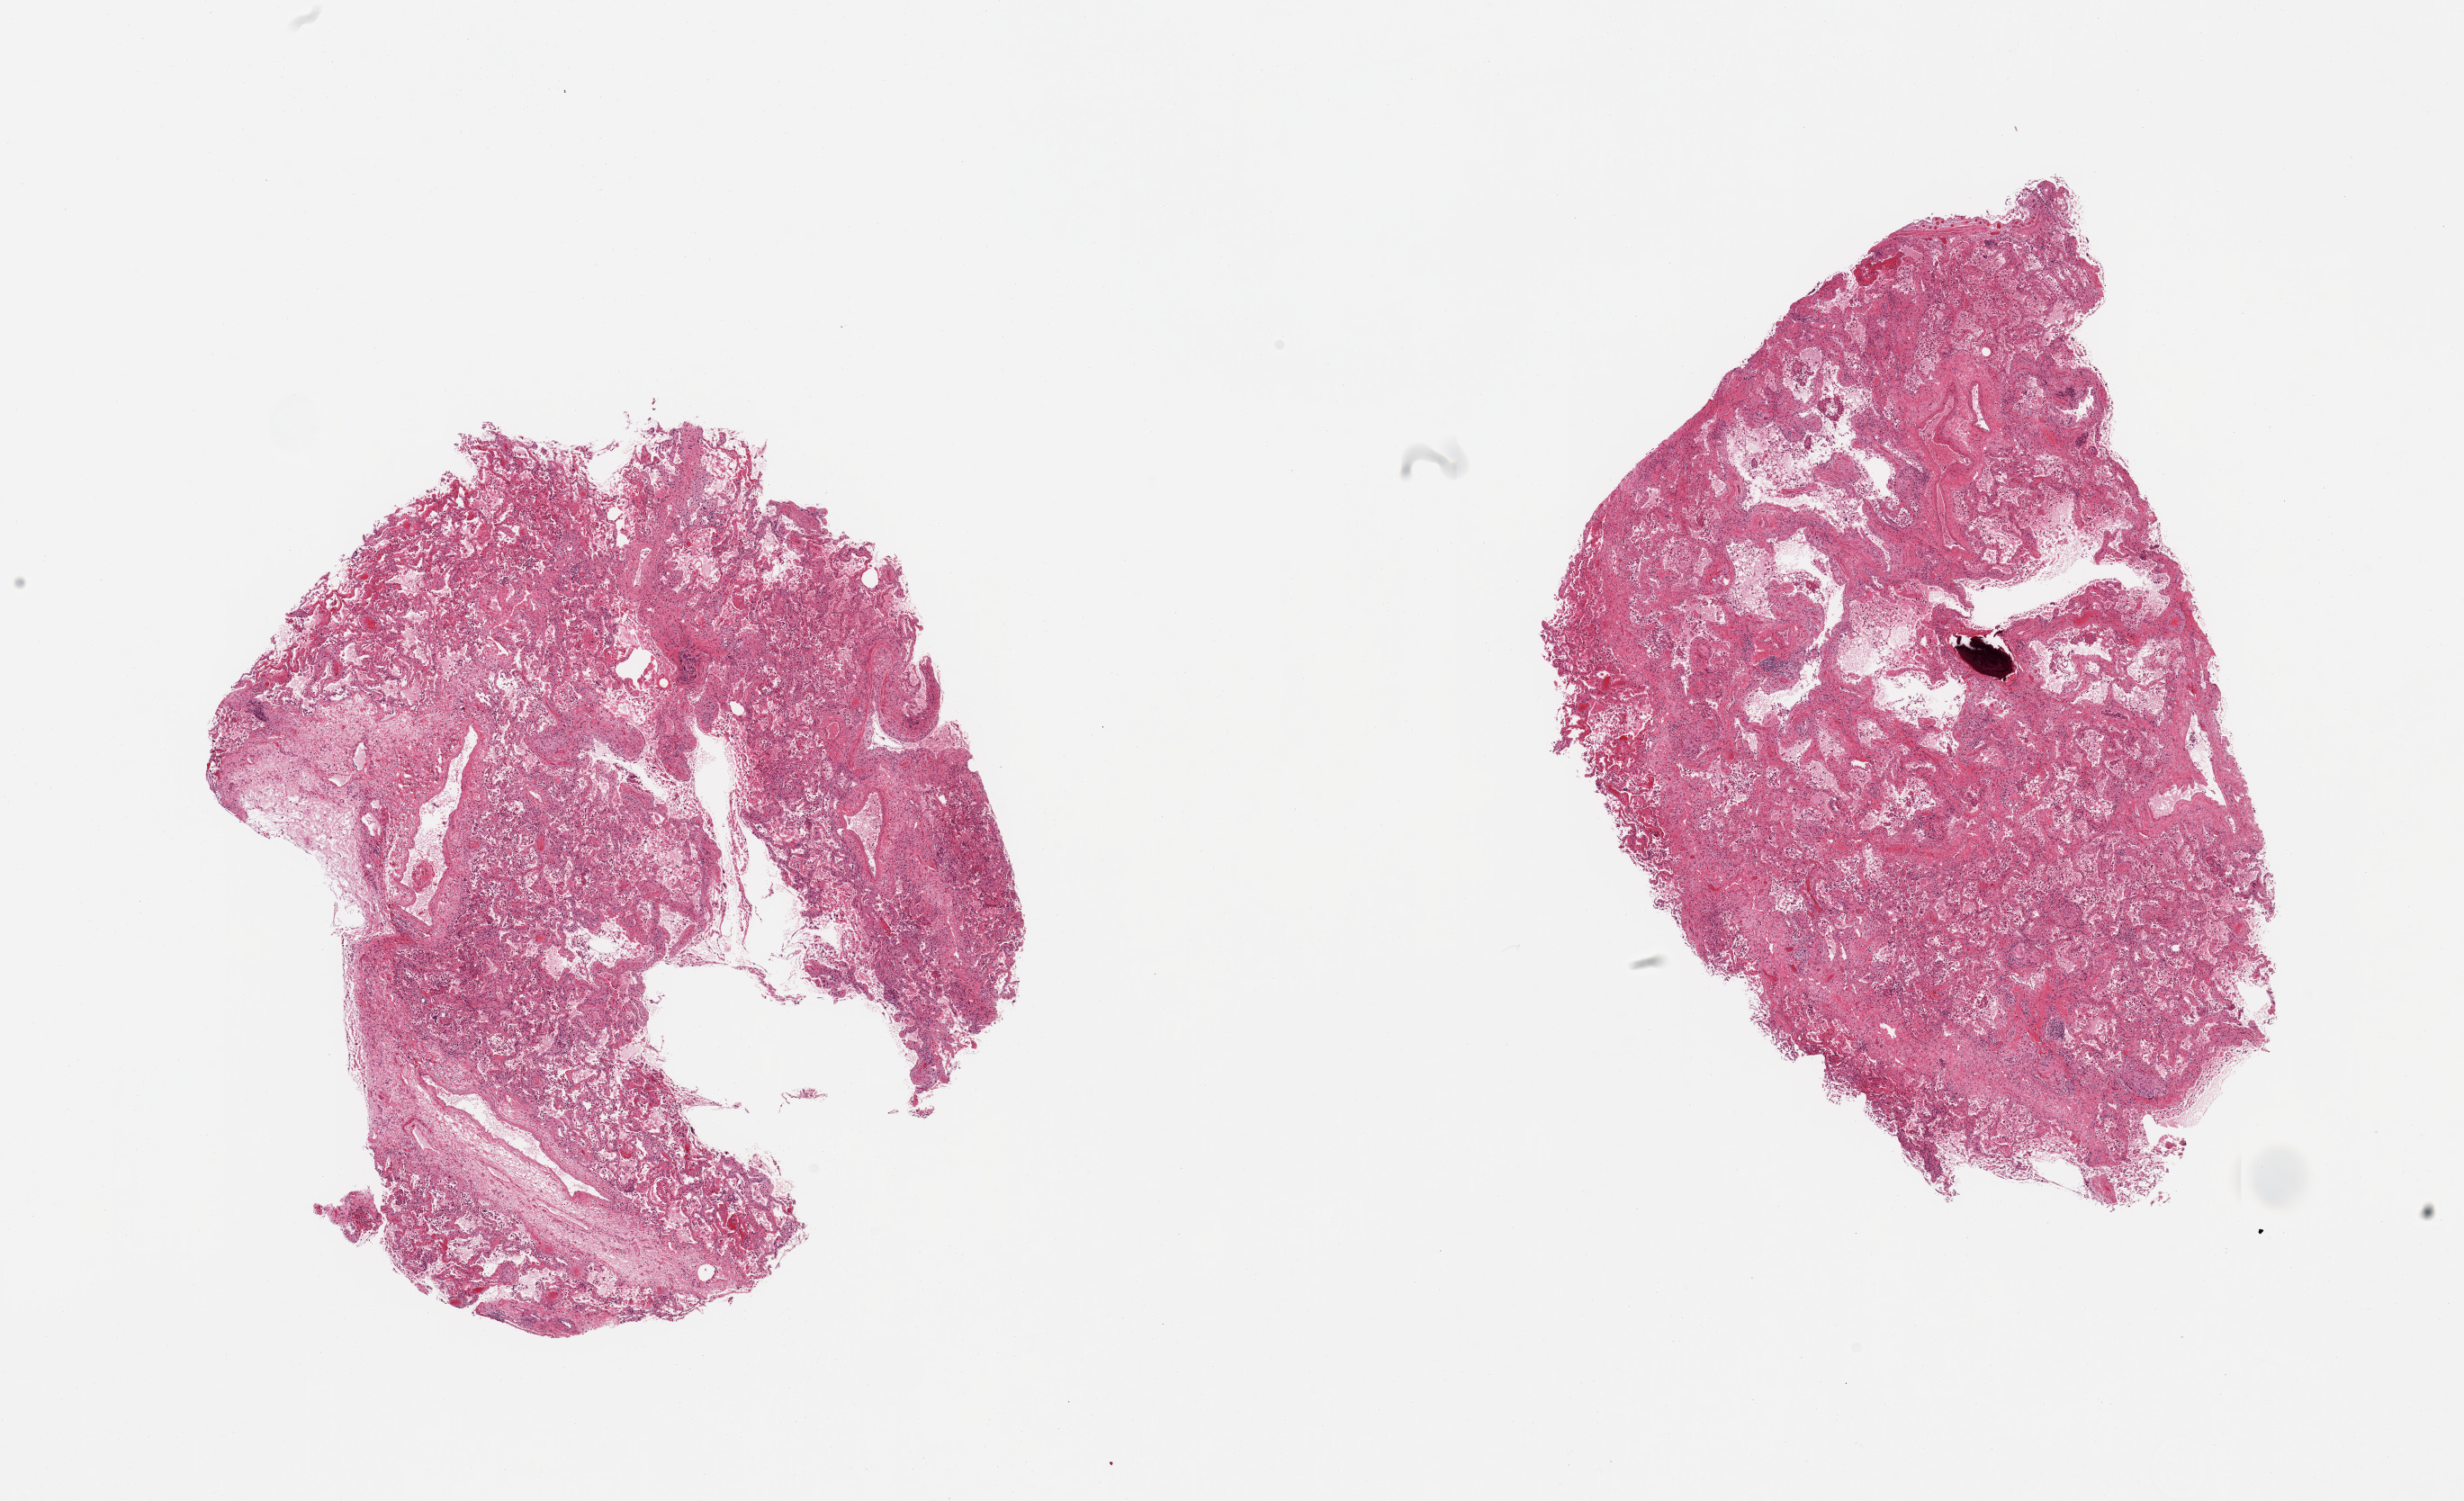
Hematoxylin and eosin (H&E) whole-slide image, brightfield — whole scanned area (about 21.7 x 13.2 mm, slide scanned at 20x) shown as a low-resolution overview. PAXgene-fixed, paraffin-embedded tissue. Sampled site (target tissue): lung. Donor tissue sample. Male donor.
Review note (as recorded): 2 pieces; alveolar macrophages, blood, desquamated cells, fluid and fibrin.